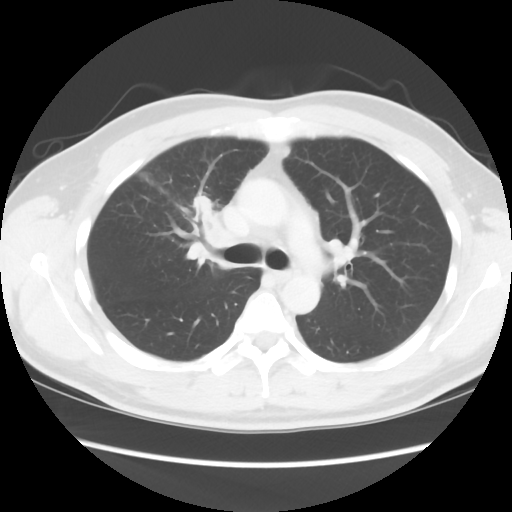
Chest CT, one axial slice; slice 60 of 80 in the series (ordered by position); reconstruction kernel STANDARD; lung window (W 1500 / L -600 HU); 5 mm slice thickness; 512 × 512 image matrix, field of view 360 × 360 mm. Male patient, age 35 years. From the clinical record (not read from this slice): clinical TNM (as recorded): T1c N1 M1b.
Outlined on this slice (bounding box drawn by a radiologist):
- lung tumour (recorded histology: adenocarcinoma): bounding box (x1, y1, x2, y2) in pixels: (189, 186, 238, 256)